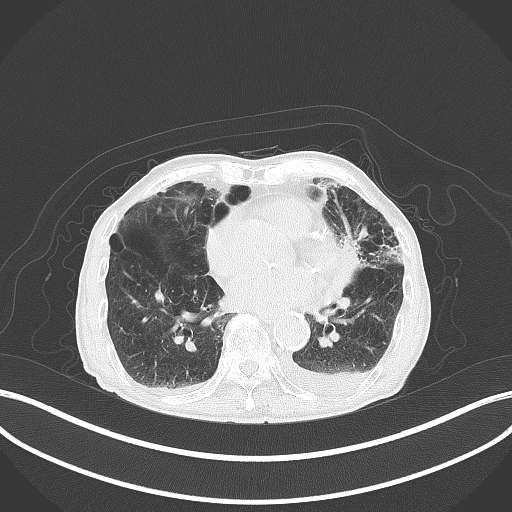
Chest CT, one axial slice. Position 177 of 227 along the scan axis. Reconstruction kernel B70f. 120 kVp. Lung window (W 1500 / L -600 HU). 3 mm slice thickness. 512 × 512 image matrix, field of view 400 × 400 mm. Male patient, age 90 years or older. Case-level facts recorded for this patient, not image findings: clinical TNM (as recorded): T2b N1 M0.
Structures marked on this image (rectangle marked by the reading radiologist):
- lung tumour (recorded histology: squamous cell carcinoma): bounding box [x1, y1, x2, y2] px = [336, 222, 362, 288]